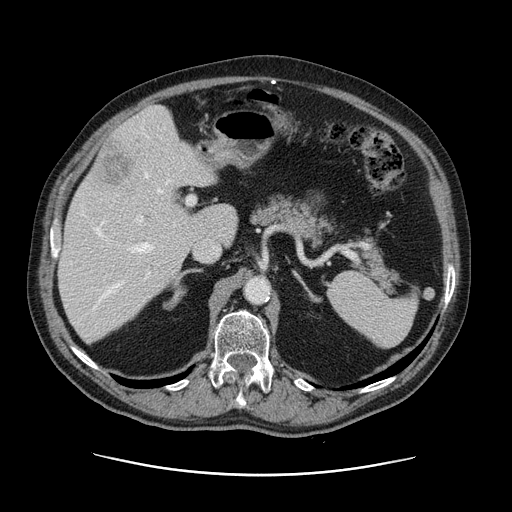
Contrast-enhanced abdominal CT, one axial slice; slice 78 of 141 in the series (ordered by position); 120 kVp; intravenous contrast given; soft-tissue window (W 400 / L 40 HU); 512 × 512 image matrix, field of view 395 × 395 mm. Male patient, age 72 years. From the clinical record (not read from this slice): diagnosis: colorectal cancer liver metastases, imaged before liver resection; multiple liver metastases: yes; largest metastasis: 5.4 cm; disease in both lobes: yes.
Outlined on this slice (outlined manually by an expert reader):
- hepatic veins: box from (x=94, y=128) to (x=170, y=308) px
- liver: (x=57, y=106)–(x=238, y=343)
- planned liver remnant (the part of the liver to remain after resection): (x=58, y=152)–(x=238, y=343)
- portal vein (with intrahepatic branches): (x=95, y=196)–(x=195, y=293)
- liver metastasis: (x=100, y=142)–(x=136, y=188)